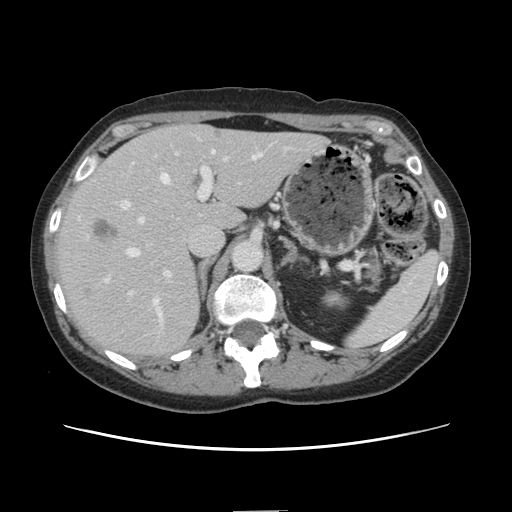
Contrast-enhanced abdominal CT, one axial slice. Slice 90 of 141 in the series (ordered by position). Soft-tissue window (W 400 / L 40 HU). 2.5 mm slice thickness. 512 × 512 image matrix, field of view 350 × 350 mm. Female patient, age 63 years. From the clinical record (not read from this slice): diagnosis: colorectal cancer liver metastases, imaged before liver resection; multiple liver metastases: yes; largest metastasis: 3.2 cm.
Annotated regions visible in this slice (manually delineated by an expert):
- hepatic veins: bounding box (x1, y1, x2, y2) in pixels: (104, 151, 261, 323)
- liver: (57, 125, 326, 357)
- planned liver remnant (the part of the liver to remain after resection): (179, 126, 327, 230)
- portal vein (with intrahepatic branches): (120, 149, 231, 294)